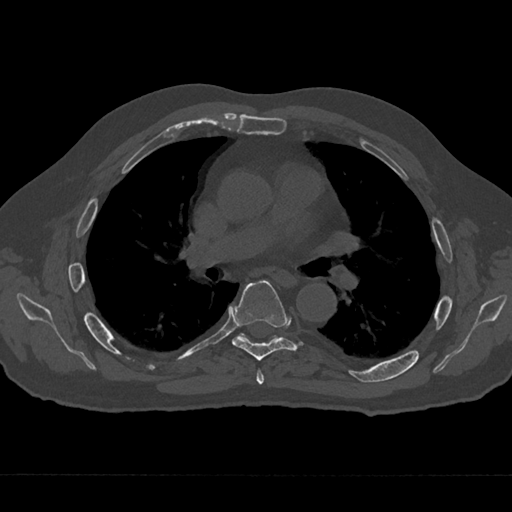
CT including the spine, one axial slice; slice 418 of 797 in the series (ordered by position); 120 kVp; bone window (W 1800 / L 400 HU); 0.5 mm slice thickness; 512 × 512 image matrix, field of view 377 × 377 mm. Patient: male, 75 years. From the clinical record (not read from this slice): primary cancer: renal; vertebrae with lytic lesions (as recorded): T4.
Structures marked on this image (semi-automatically segmented with operator editing):
- T5 vertebra: bounding box <256,369,264,385> (left, top, right, bottom; pixels)
- T6 vertebra: <232,280,303,361>